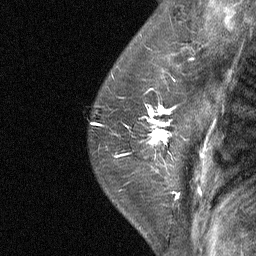
Breast MRI (dynamic contrast-enhanced), one sagittal slice. Slice 48 of 64 in the series (ordered by position). Dynamic contrast-enhanced study with each time point stored as its own series, time point 2 of 4 at this slice position (early post-contrast, ordered by acquisition time). 1.5 T. TE 4.8 ms, TR 27 ms. 2 mm slice thickness. 256 × 256 image matrix, field of view 180 × 180 mm. Patient: female, 50 years. From the clinical record (not read from this slice): setting: breast cancer imaged before/during neoadjuvant chemotherapy; receptor status: HER2-positive.
Structures marked on this image (semi-automatically segmented with operator editing):
- analysis volume of interest (the breast-tissue region the enhancement analysis was run in; not a lesion): box from (x=123, y=91) to (x=189, y=177) px
- tumour enhancement mask (voxels above the 90 % enhancement threshold inside the analysis volume of interest): (x=149, y=106)–(x=171, y=145)